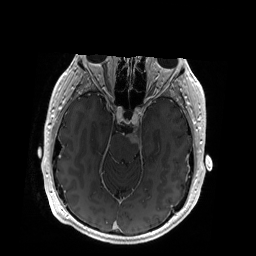
Brain MRI from a brain-tumour surgery series, one axial slice; slice 121 of 192 in the series (ordered by position); T1-weighted post-contrast; 1 mm slice thickness; 256 × 256 image matrix, field of view 256 × 256 mm. Case-level facts recorded for this patient, not image findings: histopathology: Glioblastoma; WHO grade: 4; IDH mutation: no.
Annotated regions visible in this slice (expert manual segmentation):
- tumour: bounding box [x1, y1, x2, y2] px = [128, 126, 142, 144]